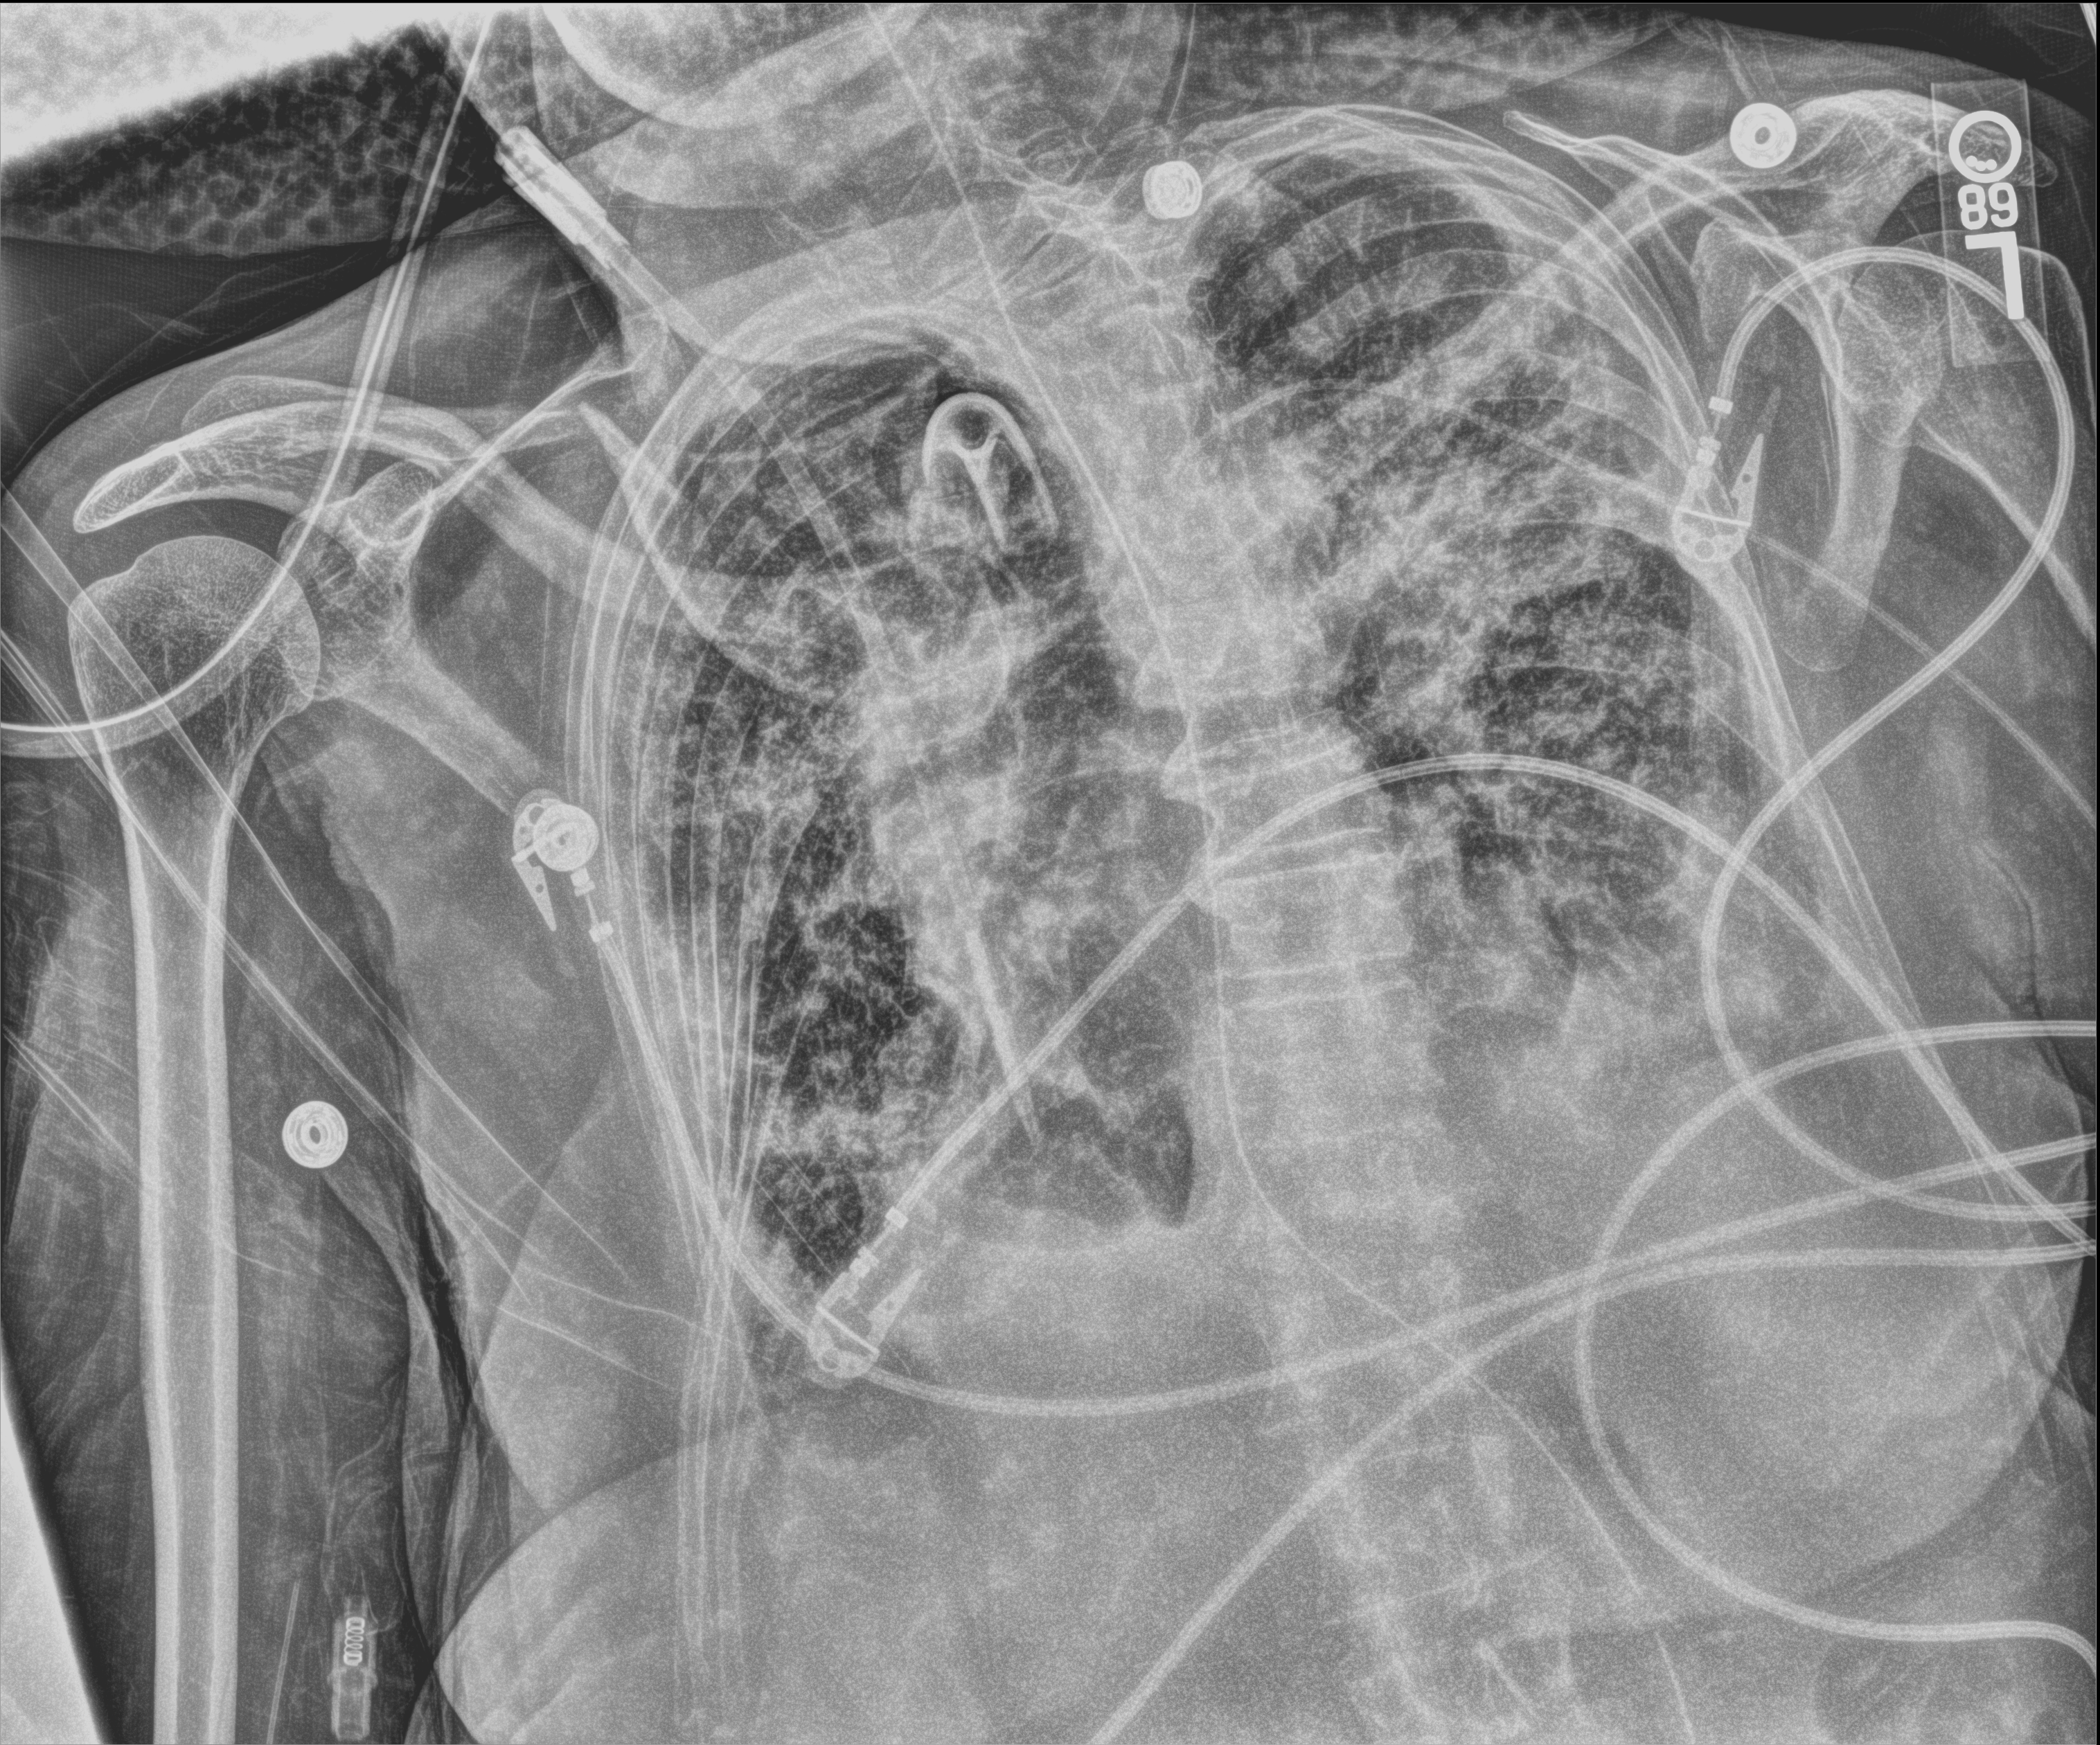
Chest X-ray (portable); anteroposterior (AP) projection. Patient hospitalised with COVID-19; female, aged 75–90 years.
Hospital-stay facts (about this admission, not read from this image; timing relative to this image not recorded):
- admitted to intensive care during this hospital stay: yes
- mechanically ventilated during this hospital stay: yes